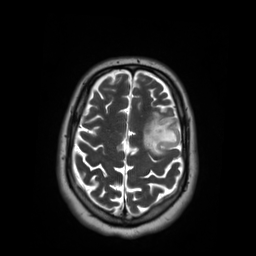
Brain MRI from a brain-tumour surgery series, one axial slice. Slice 43 of 59 in the series (ordered by position). 3.03 mm slice thickness. 256 × 256 image matrix, field of view 250 × 250 mm. Case-level facts recorded for this patient, not image findings: histopathology: Oligodendroglioma; WHO grade: 2; IDH mutation: yes.
Outlined on this slice (manually delineated by an expert):
- tumour: box from (x=139, y=110) to (x=180, y=155) px